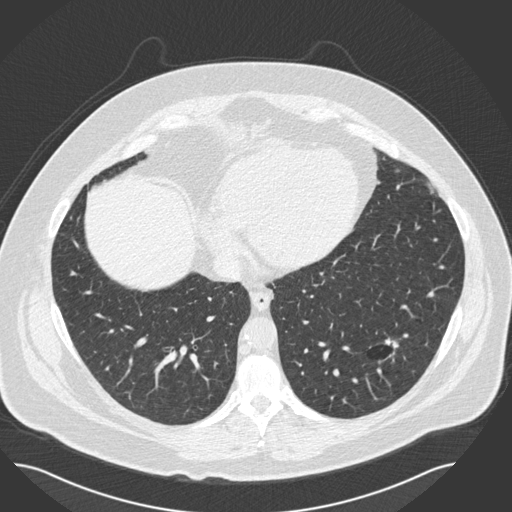
Chest CT (low-dose screening protocol), one axial image; second screening round (one year after baseline); lung window (W 1500 / L -600 HU); 2 mm slice thickness; standard (soft-tissue) reconstruction kernel (B30f); 512 × 512 image matrix. Male, age 57 years at enrolment. Current smoker at enrolment.
• Lesion marked by an expert reader, bounding box [x1, y1, x2, y2] px = [358, 322, 425, 383].
• Reader record for this screening exam (exam-level; its link to the box is not recorded): non-calcified nodule or mass ≥4 mm, left lower lobe, 19 × 15 mm, pre-existing on the prior screen: yes; interval growth: no.
• Later outcome: lung cancer diagnosed 434 days after this screen (after the third annual screen) — squamous cell carcinoma, NOS, left lower lobe, moderately differentiated (G2), stage IA (AJCC 6th edition), 22 mm at pathology.